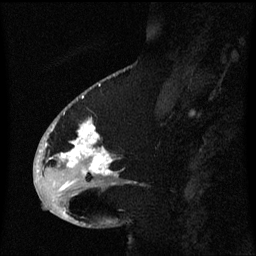
Breast MRI (dynamic contrast-enhanced), one sagittal slice. Slice 26 of 60 in the series (ordered by position). Dynamic contrast-enhanced series, image 2 of 3 at this slice position (ordered by acquisition). 1.5 T. TE 4.2 ms, TR 8.4 ms. 2.1 mm slice thickness. 256 × 256 image matrix. Female patient, age 53 years. Case-level facts recorded for this patient, not image findings: setting: breast cancer imaged before/during neoadjuvant chemotherapy; receptor status: HR-positive, HER2-negative.
Structures marked on this image (semi-automatically segmented with operator editing):
- analysis volume of interest (the breast-tissue region the enhancement analysis was run in; not a lesion): bounding box [x1, y1, x2, y2] px = [49, 108, 133, 201]
- tumour enhancement mask (voxels above the 70 % enhancement threshold inside the analysis volume of interest): [60, 120, 114, 175]